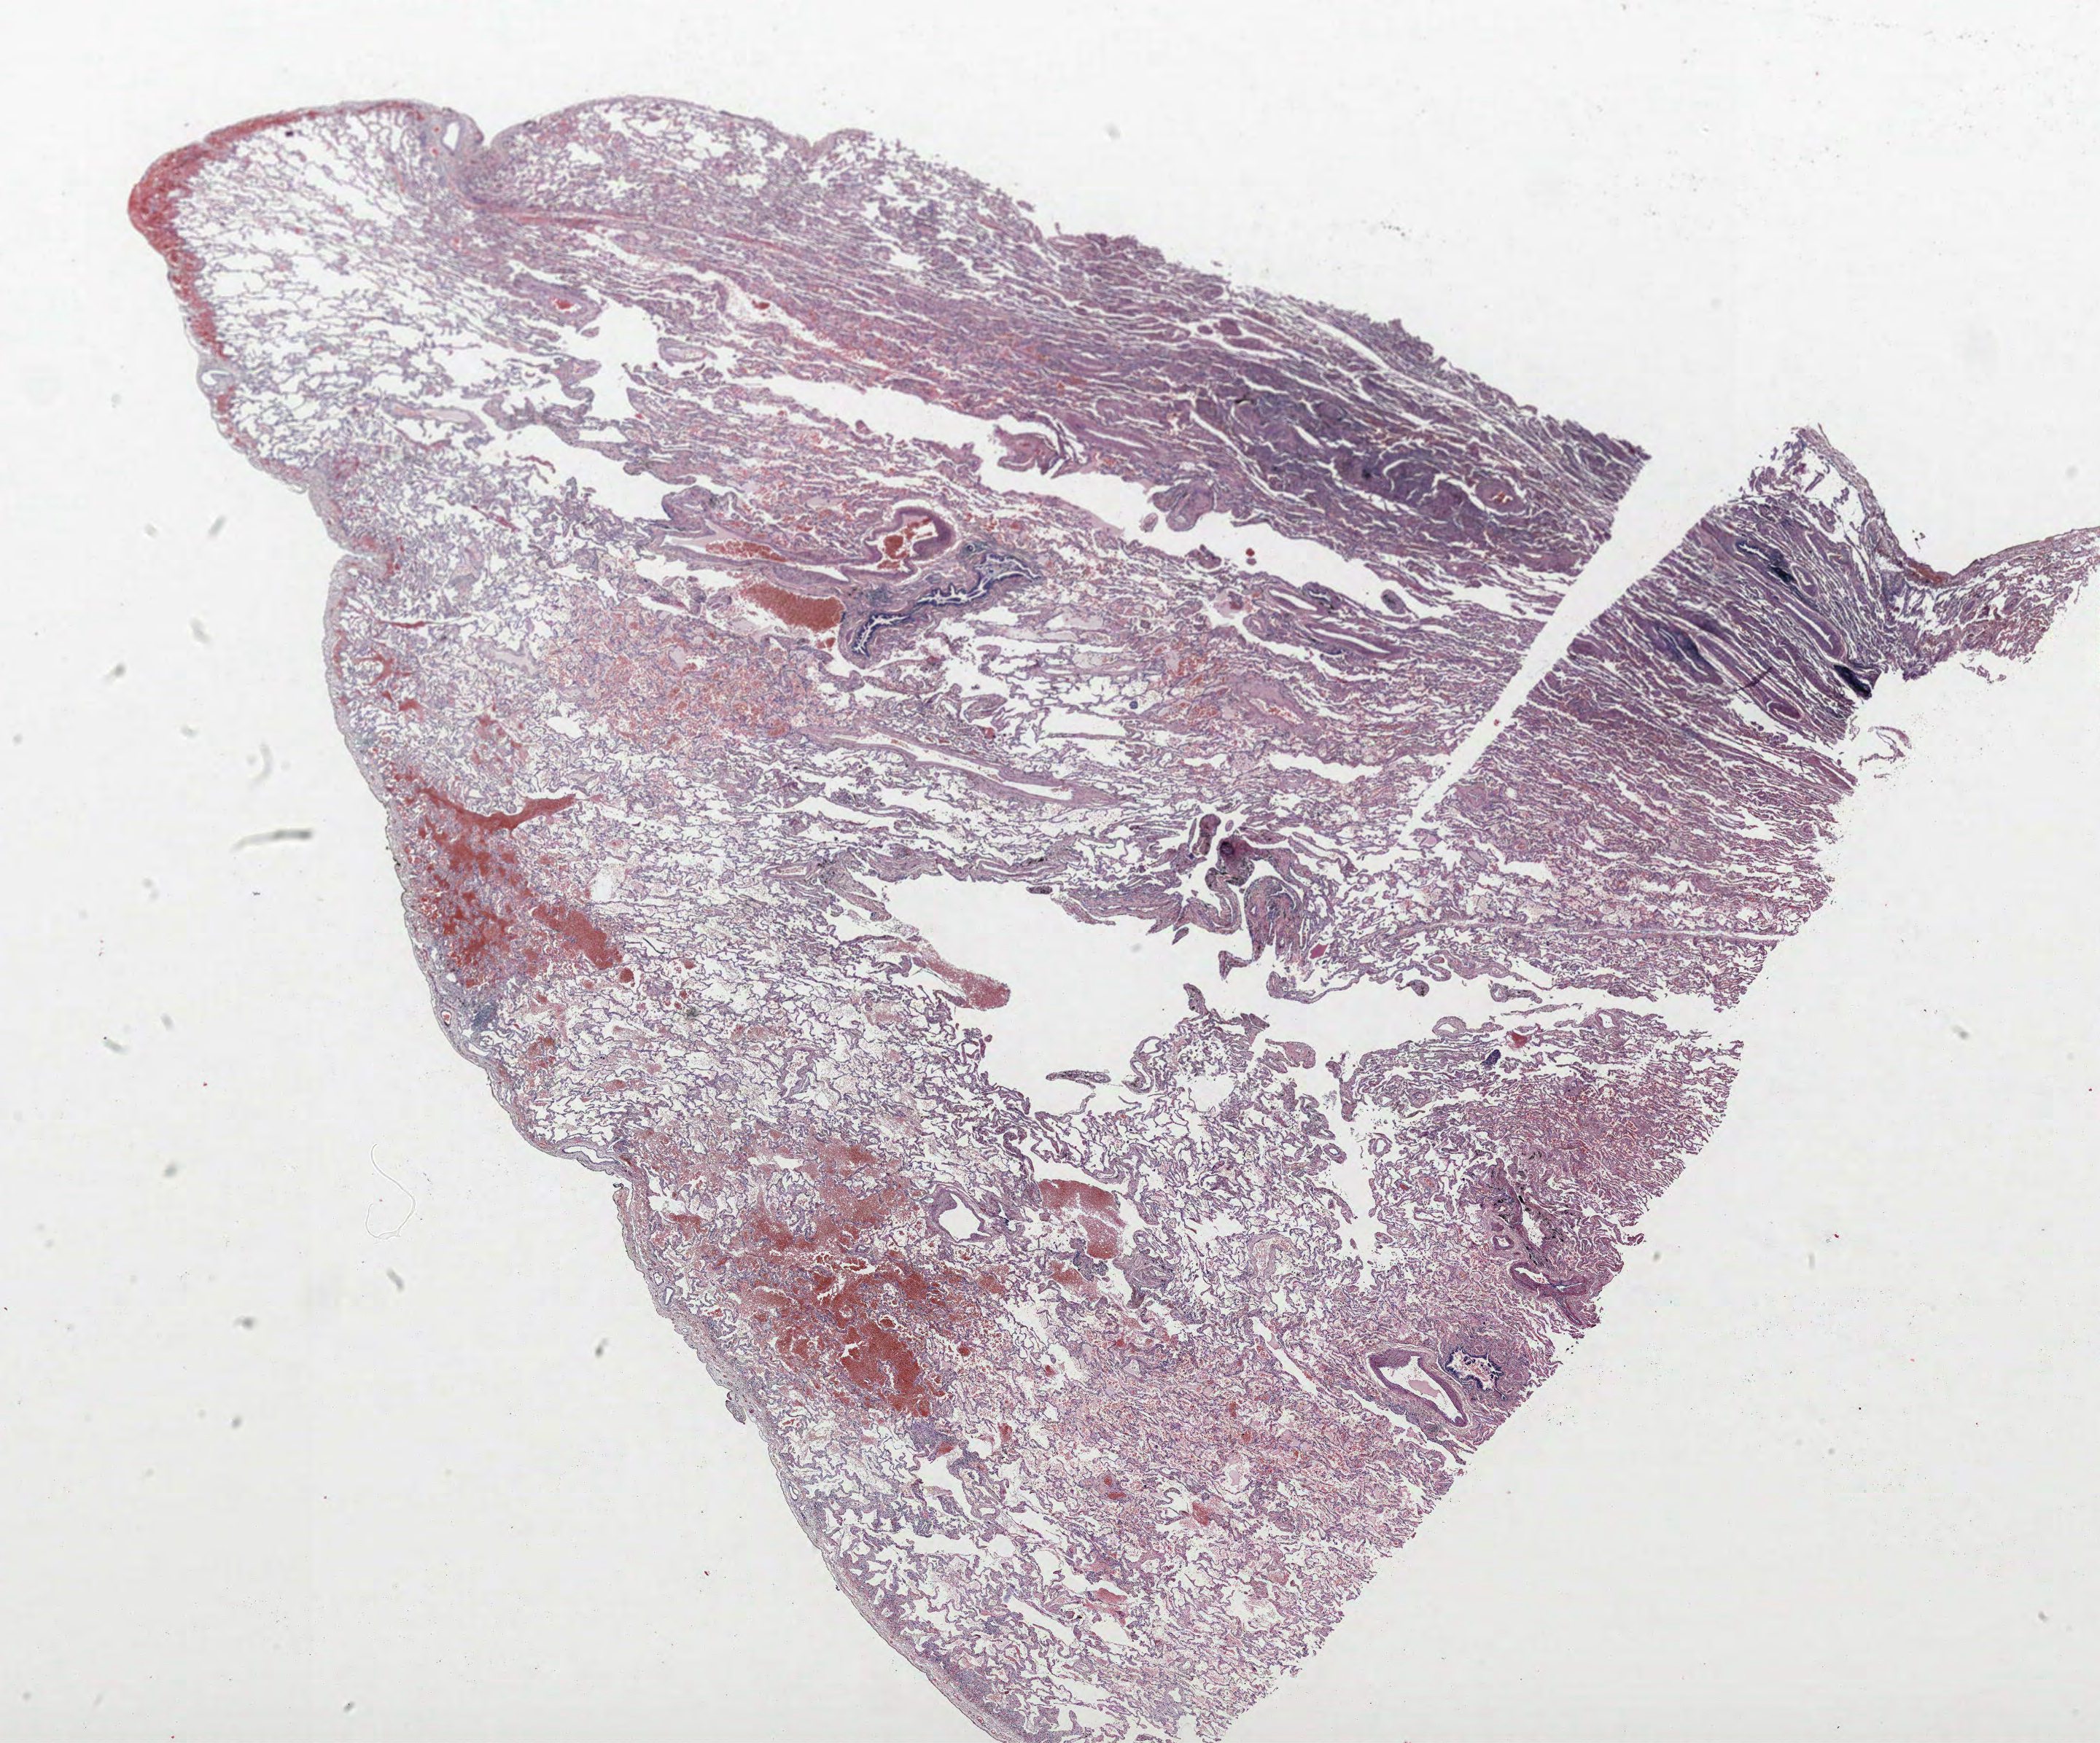
Hematoxylin and eosin (H&E) stained whole-slide image — shown as a low-resolution overview of the whole scanned area (about 23.0 x 19.1 mm, acquisition: 40x scan); formalin-fixed paraffin-embedded (FFPE) section; lung. Male patient, aged 64 at enrolment.
Participant's lung-cancer diagnosis: Squamous cell carcinoma, NOS (ICD-O-3 8070/3).